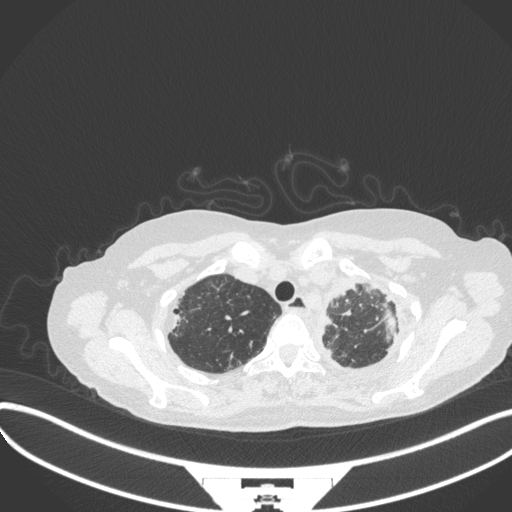
Chest CT, one axial slice; position 292 of 373 along the scan axis; reconstruction kernel B31f; lung window (W 1500 / L -600 HU); 1 mm slice thickness; 512 × 512 image matrix, field of view 400 × 400 mm. Female patient, age 56 years. Case-level facts recorded for this patient, not image findings: clinical TNM (as recorded): T1 N0 M0.
Outlined on this slice (bounding box drawn by a radiologist):
- lung tumour (recorded histology: adenocarcinoma): bounding box <378,300,397,340> (left, top, right, bottom; pixels)